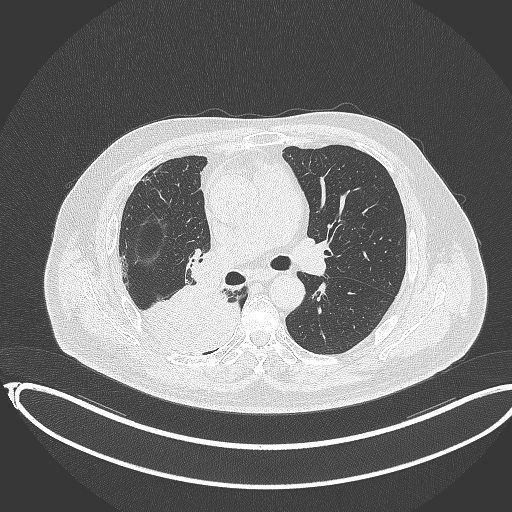
Chest CT, one axial slice. Slice 207 of 403 in the series (ordered by position). Reconstruction kernel B70f. 120 kVp. Lung window (W 1500 / L -600 HU). 1 mm slice thickness. 512 × 512 image matrix, field of view 436 × 436 mm. Patient: male, 68 years. Case-level facts recorded for this patient, not image findings: clinical TNM (as recorded): T2a N0 M0.
Outlined on this slice (rectangle marked by the reading radiologist):
- lung tumour (recorded histology: adenocarcinoma): bounding box (x1, y1, x2, y2) in pixels: (145, 284, 244, 350)